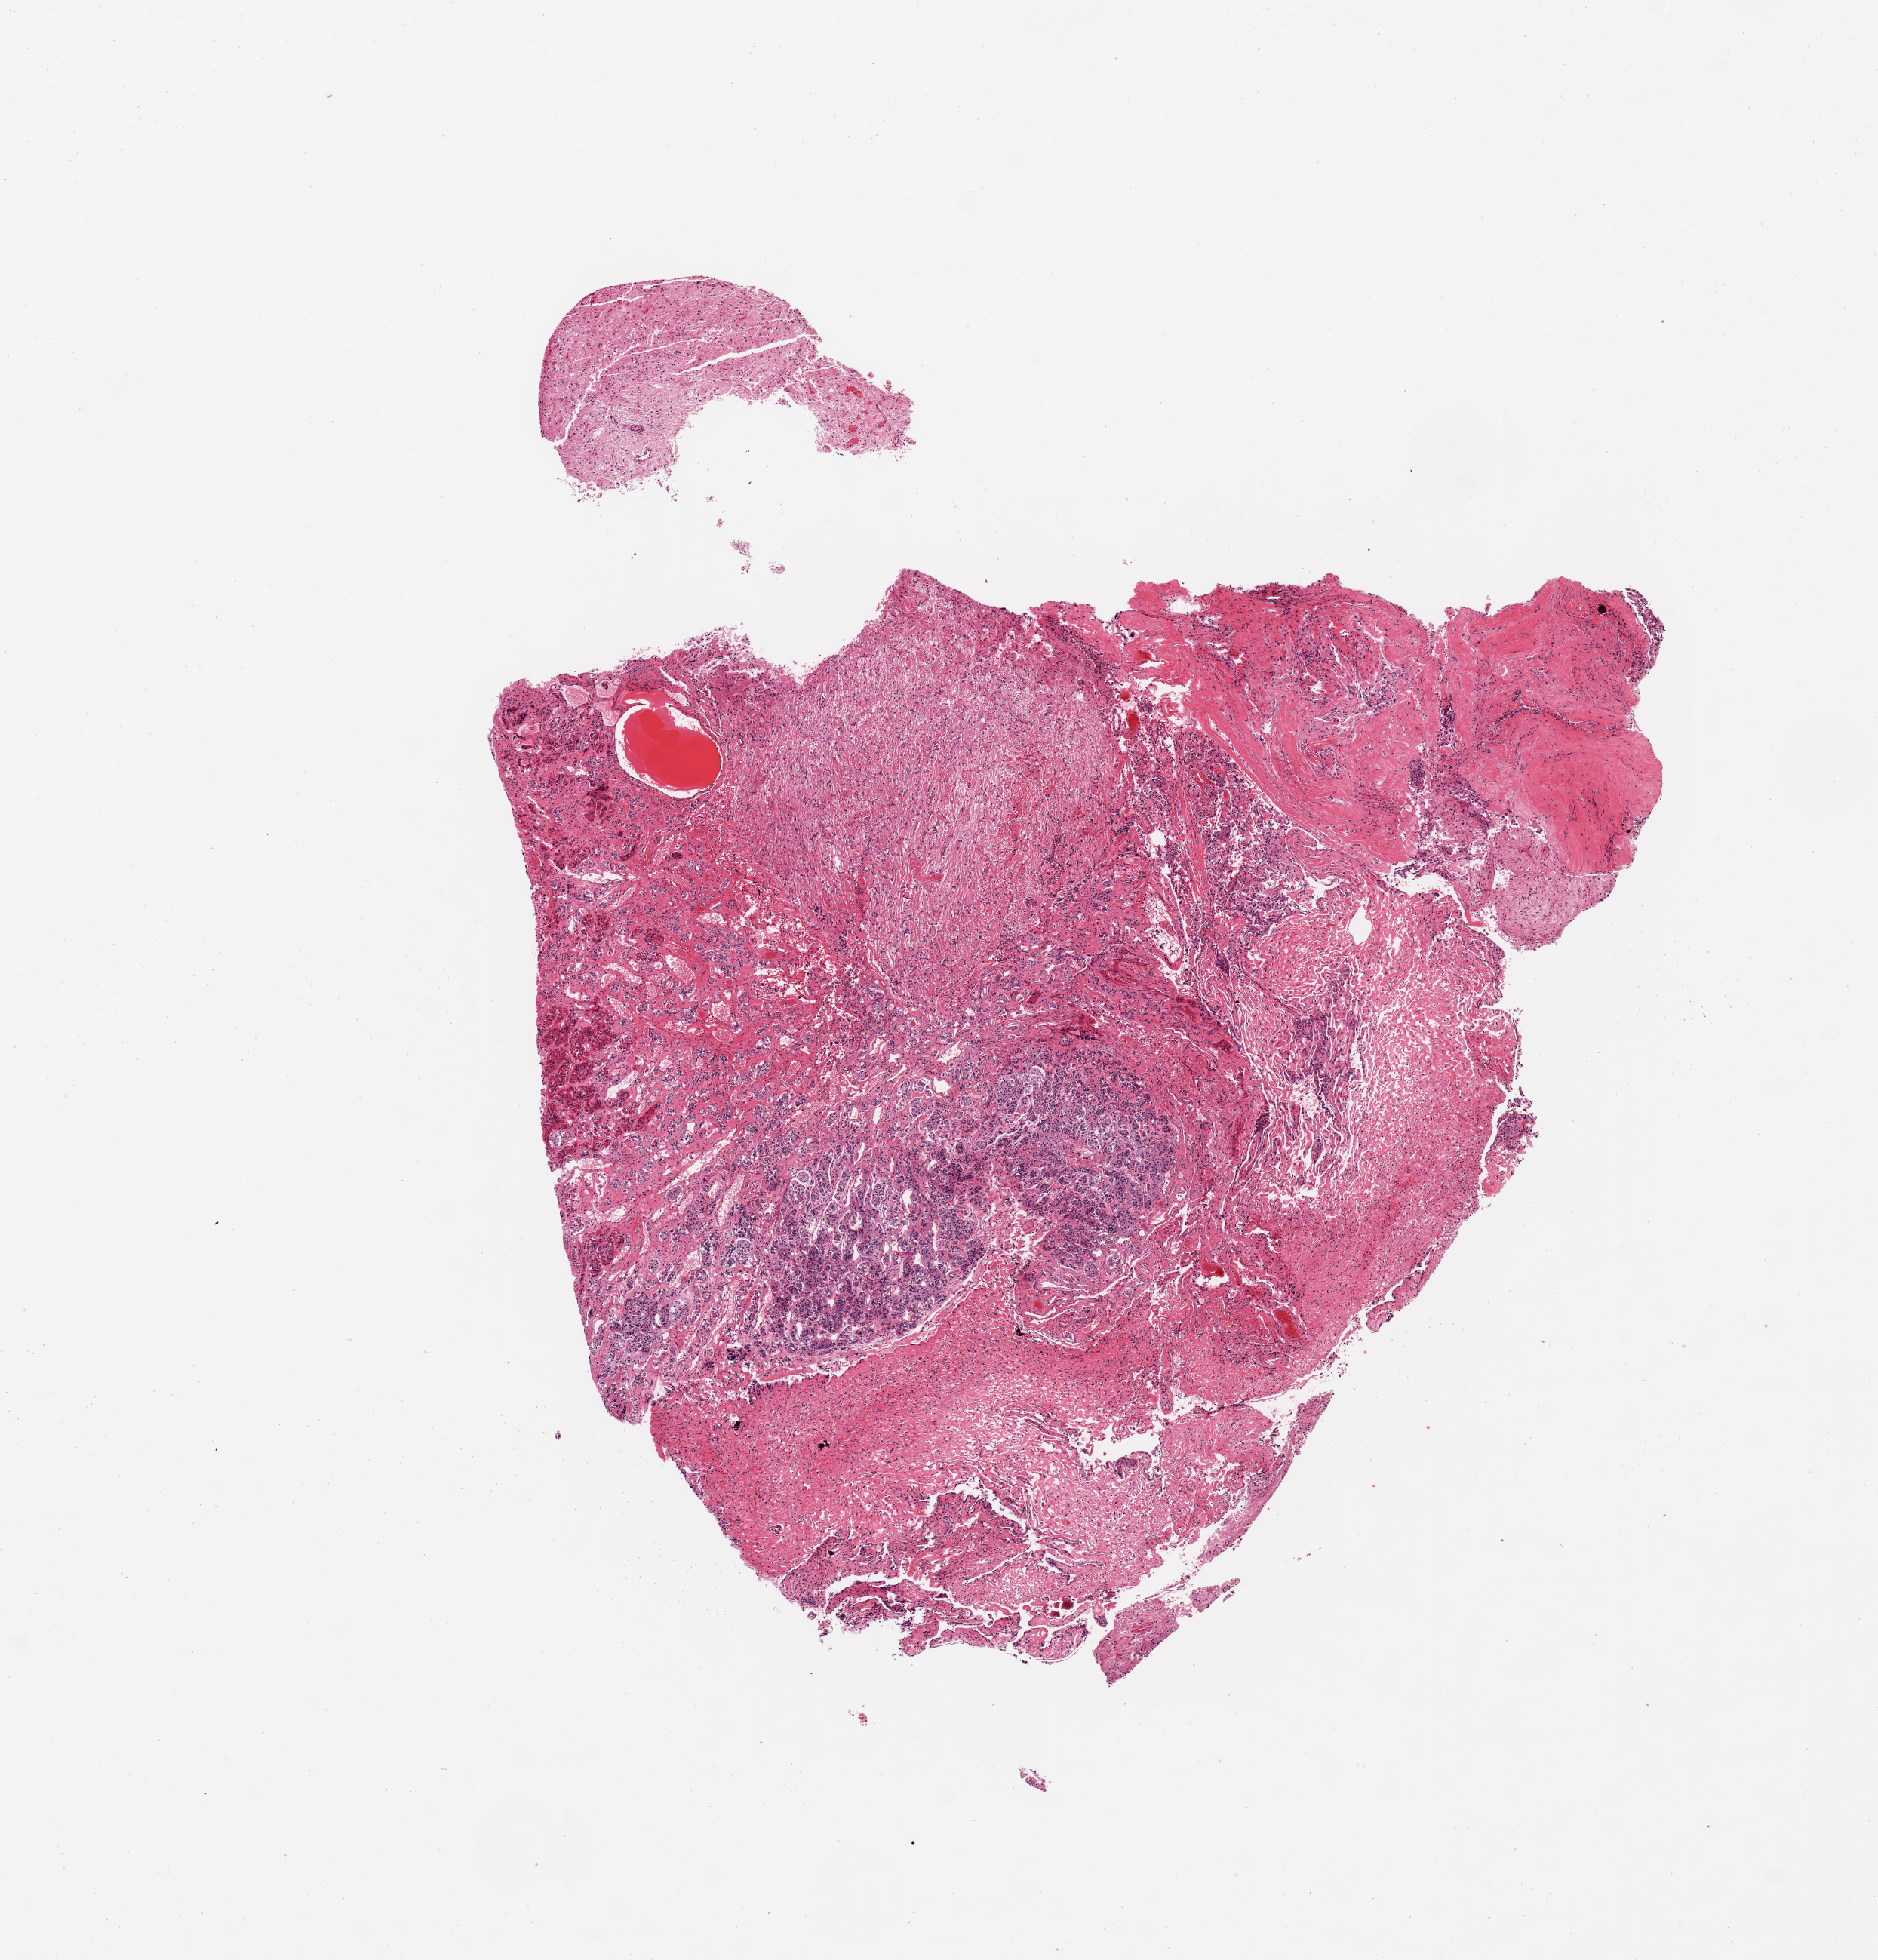
Digitized H&E-stained section, whole scanned area (about 9.8 x 10.3 mm, acquisition: 20x scan) shown as a low-resolution overview. PAXgene-fixed paraffin-embedded (PFPE) section. Target tissue: pituitary. Tissue donor sample.
• reviewer comment on this tissue sample: 1 piece, commingled adeno-and neuro-hypophysis; Small adherent nubbin of dura, ~3x2mm, also